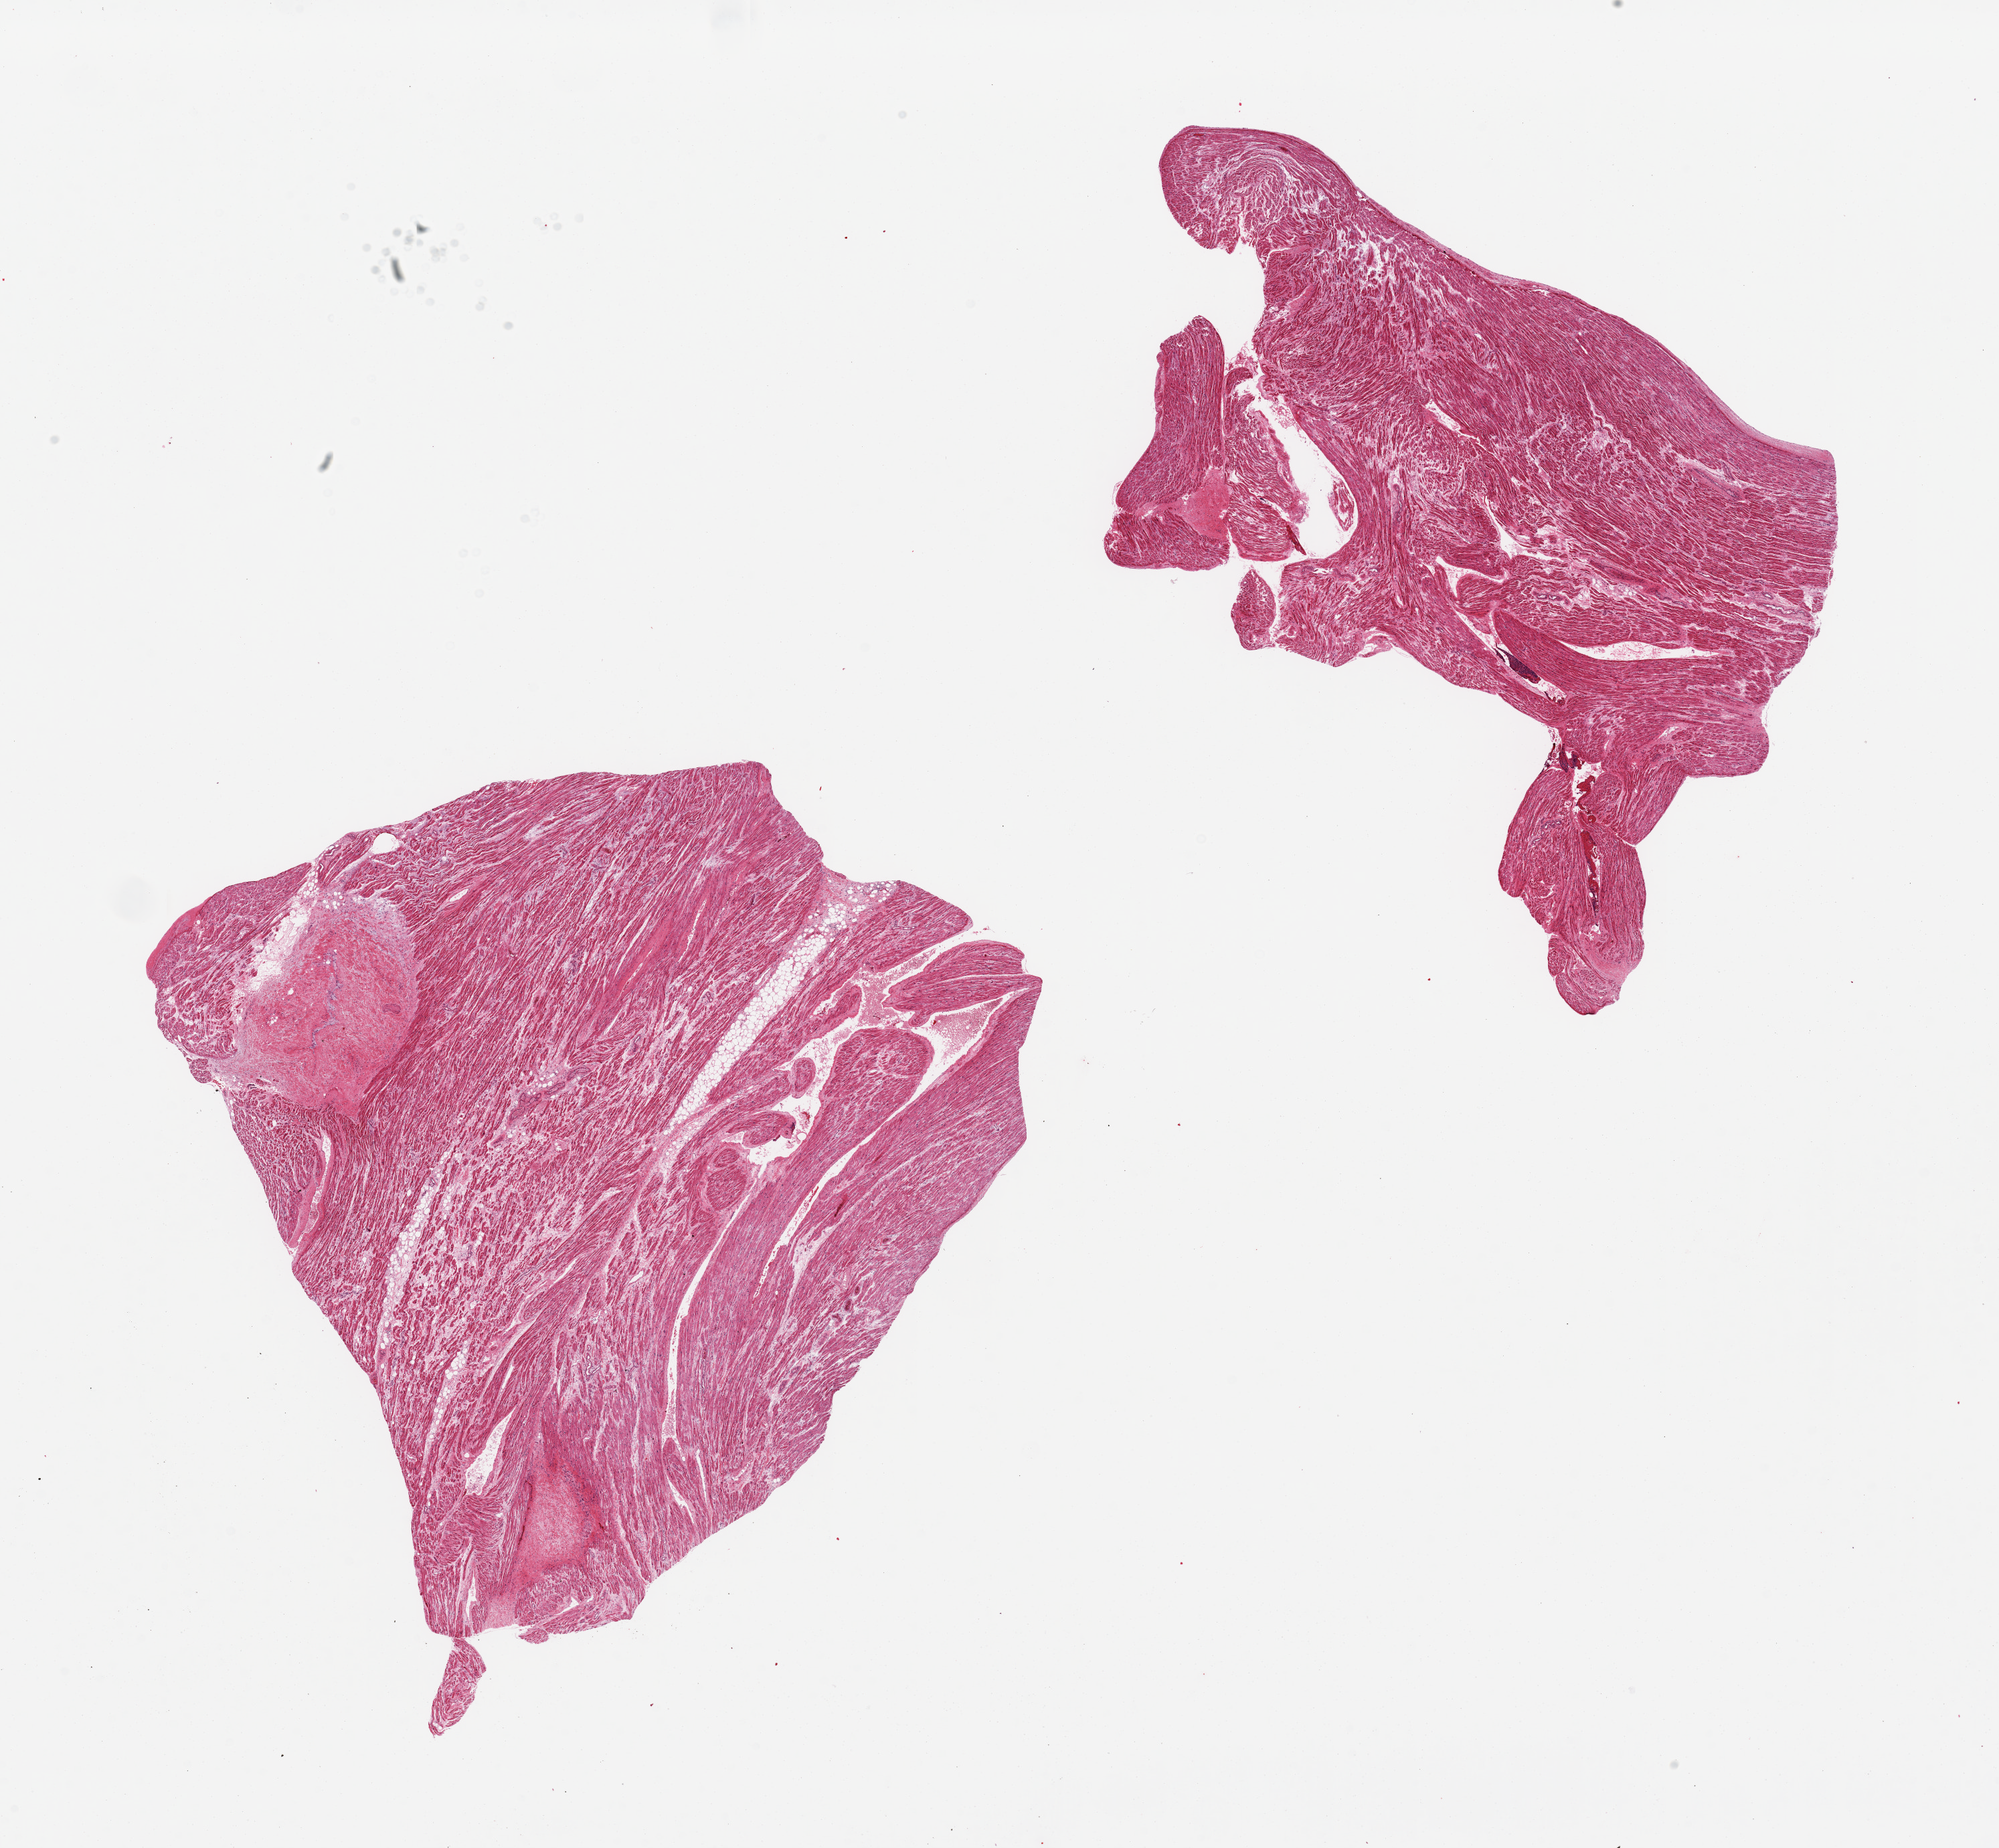
Whole-slide image, hematoxylin and eosin (H&E) stain, brightfield — shown as a low-resolution overview of the whole scanned area (about 23.6 x 21.8 mm, slide scanned at 20x); PAXgene-fixed, paraffin-embedded tissue; sampled site (target tissue): auricular appendage; donor tissue sample. Female donor.
Pathologist's review note for this sample: 2 pieces.